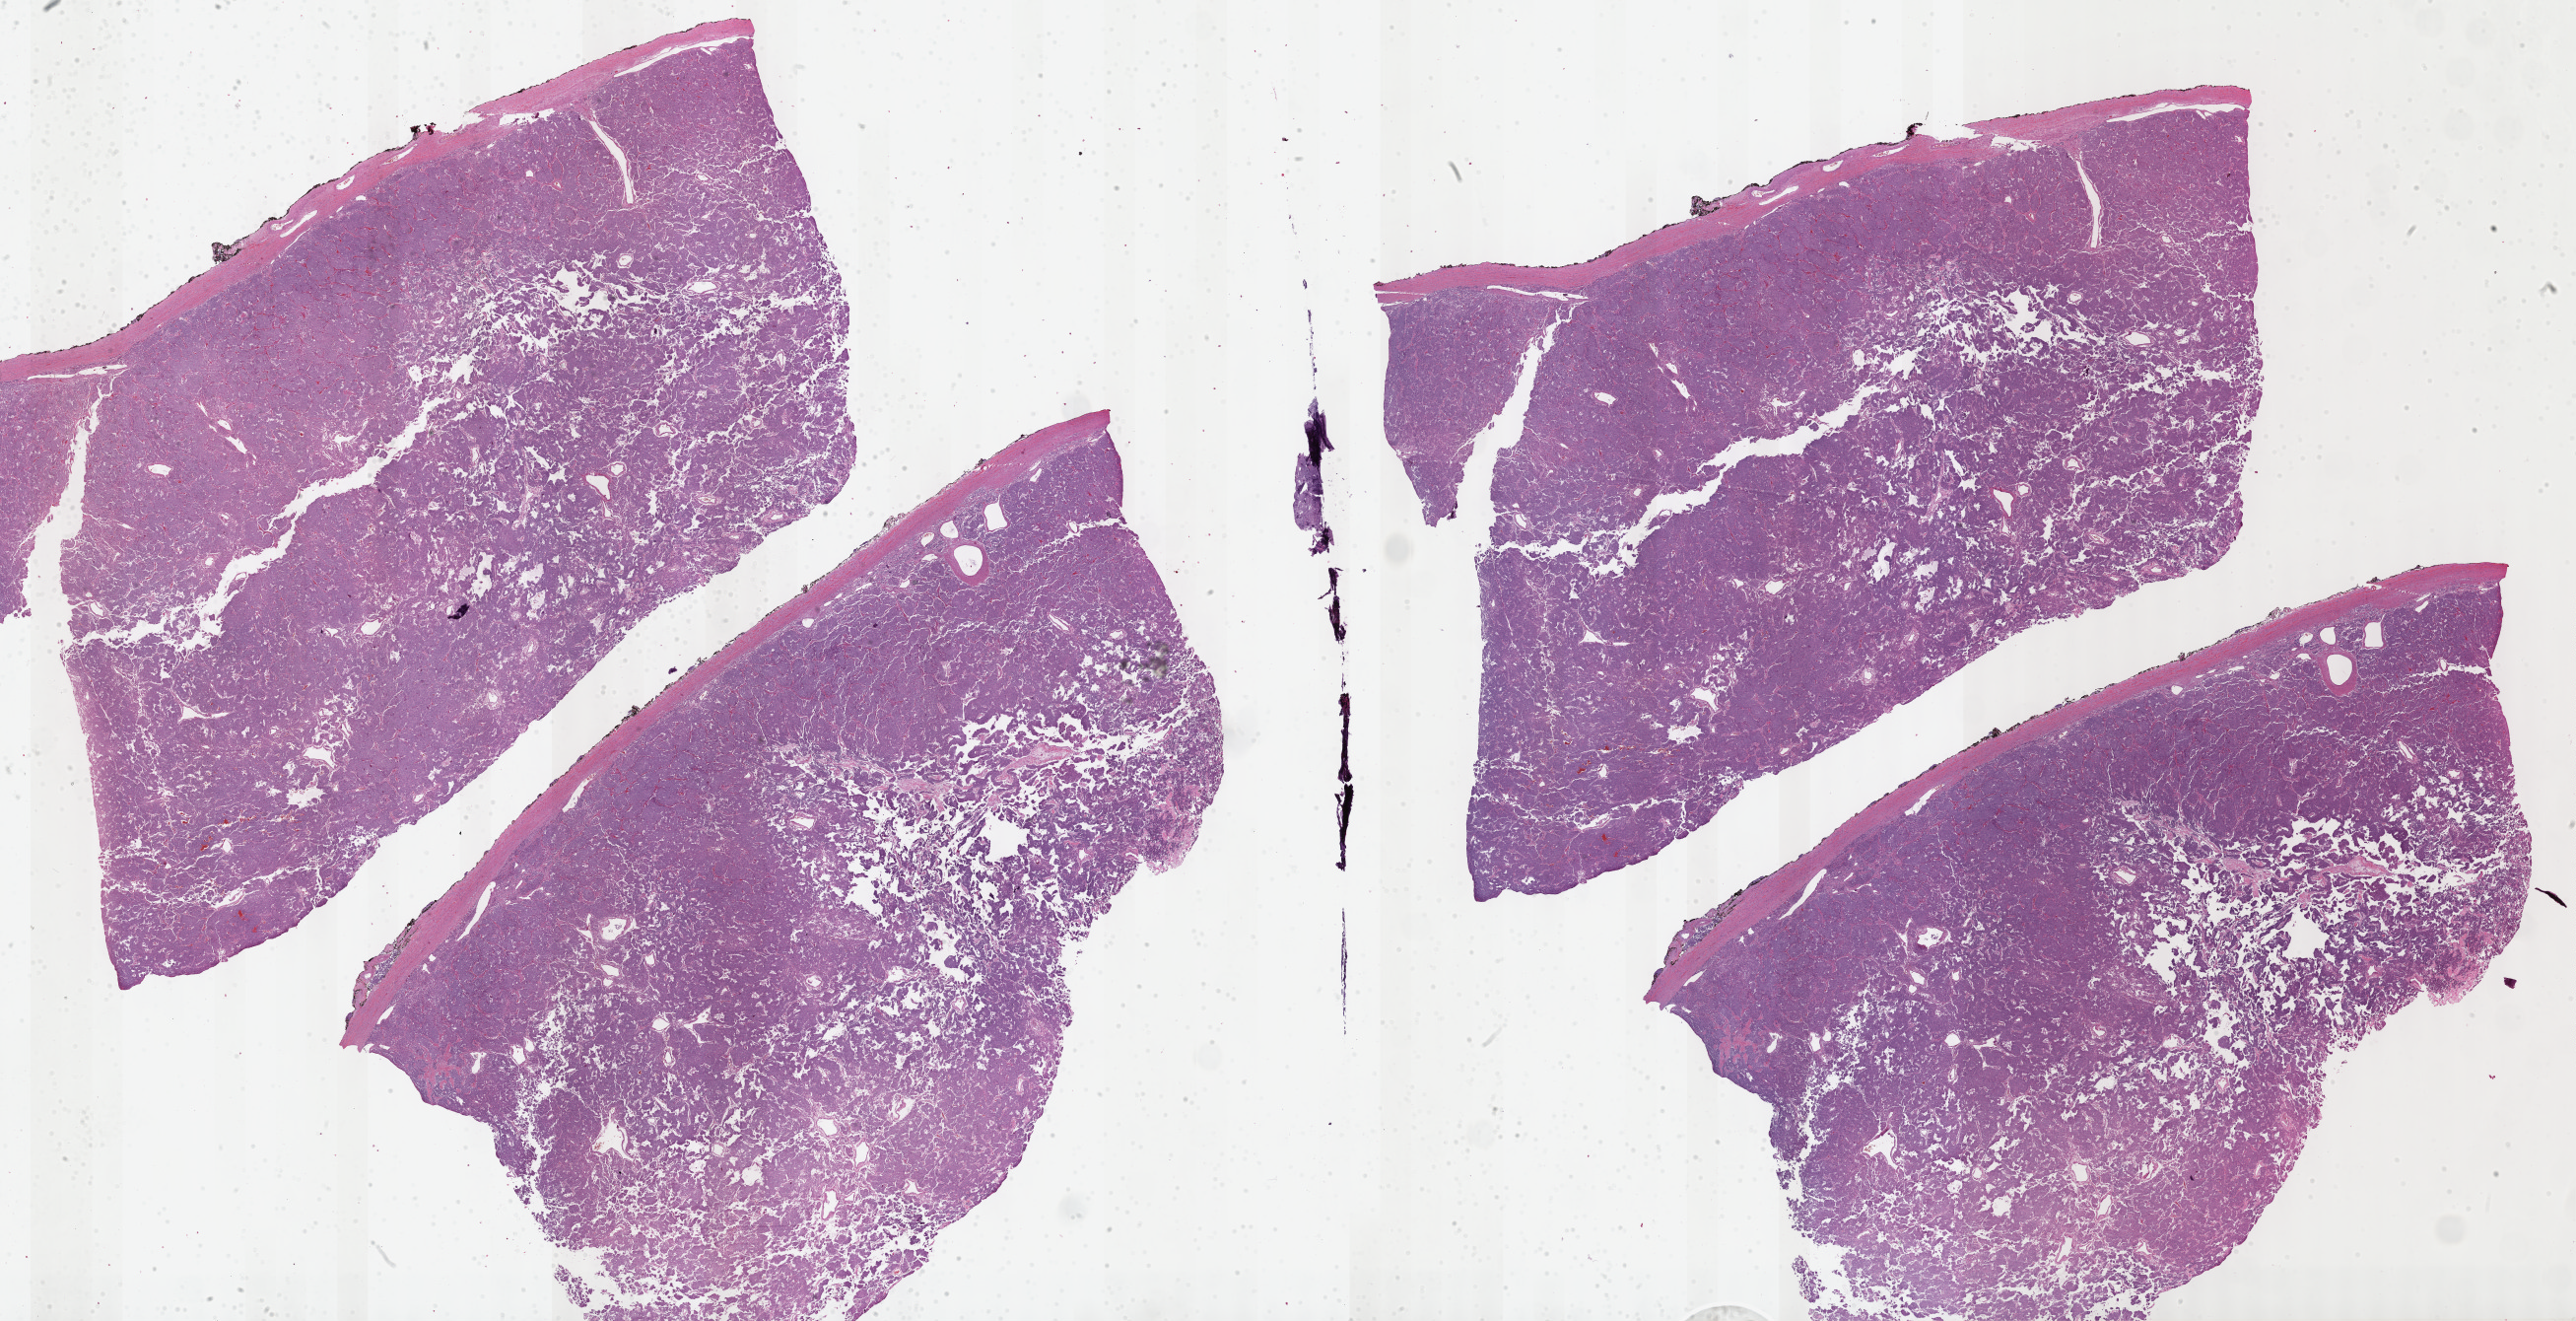
Whole-slide histology image, H&E, whole scanned area (about 42.3 x 21.7 mm) shown as a low-resolution overview; formalin-fixed paraffin-embedded (FFPE) diagnostic section; sample: primary tumour, adrenal gland. Female patient; age at initial diagnosis 53 years.
Diagnosis: Pheochromocytoma, NOS.